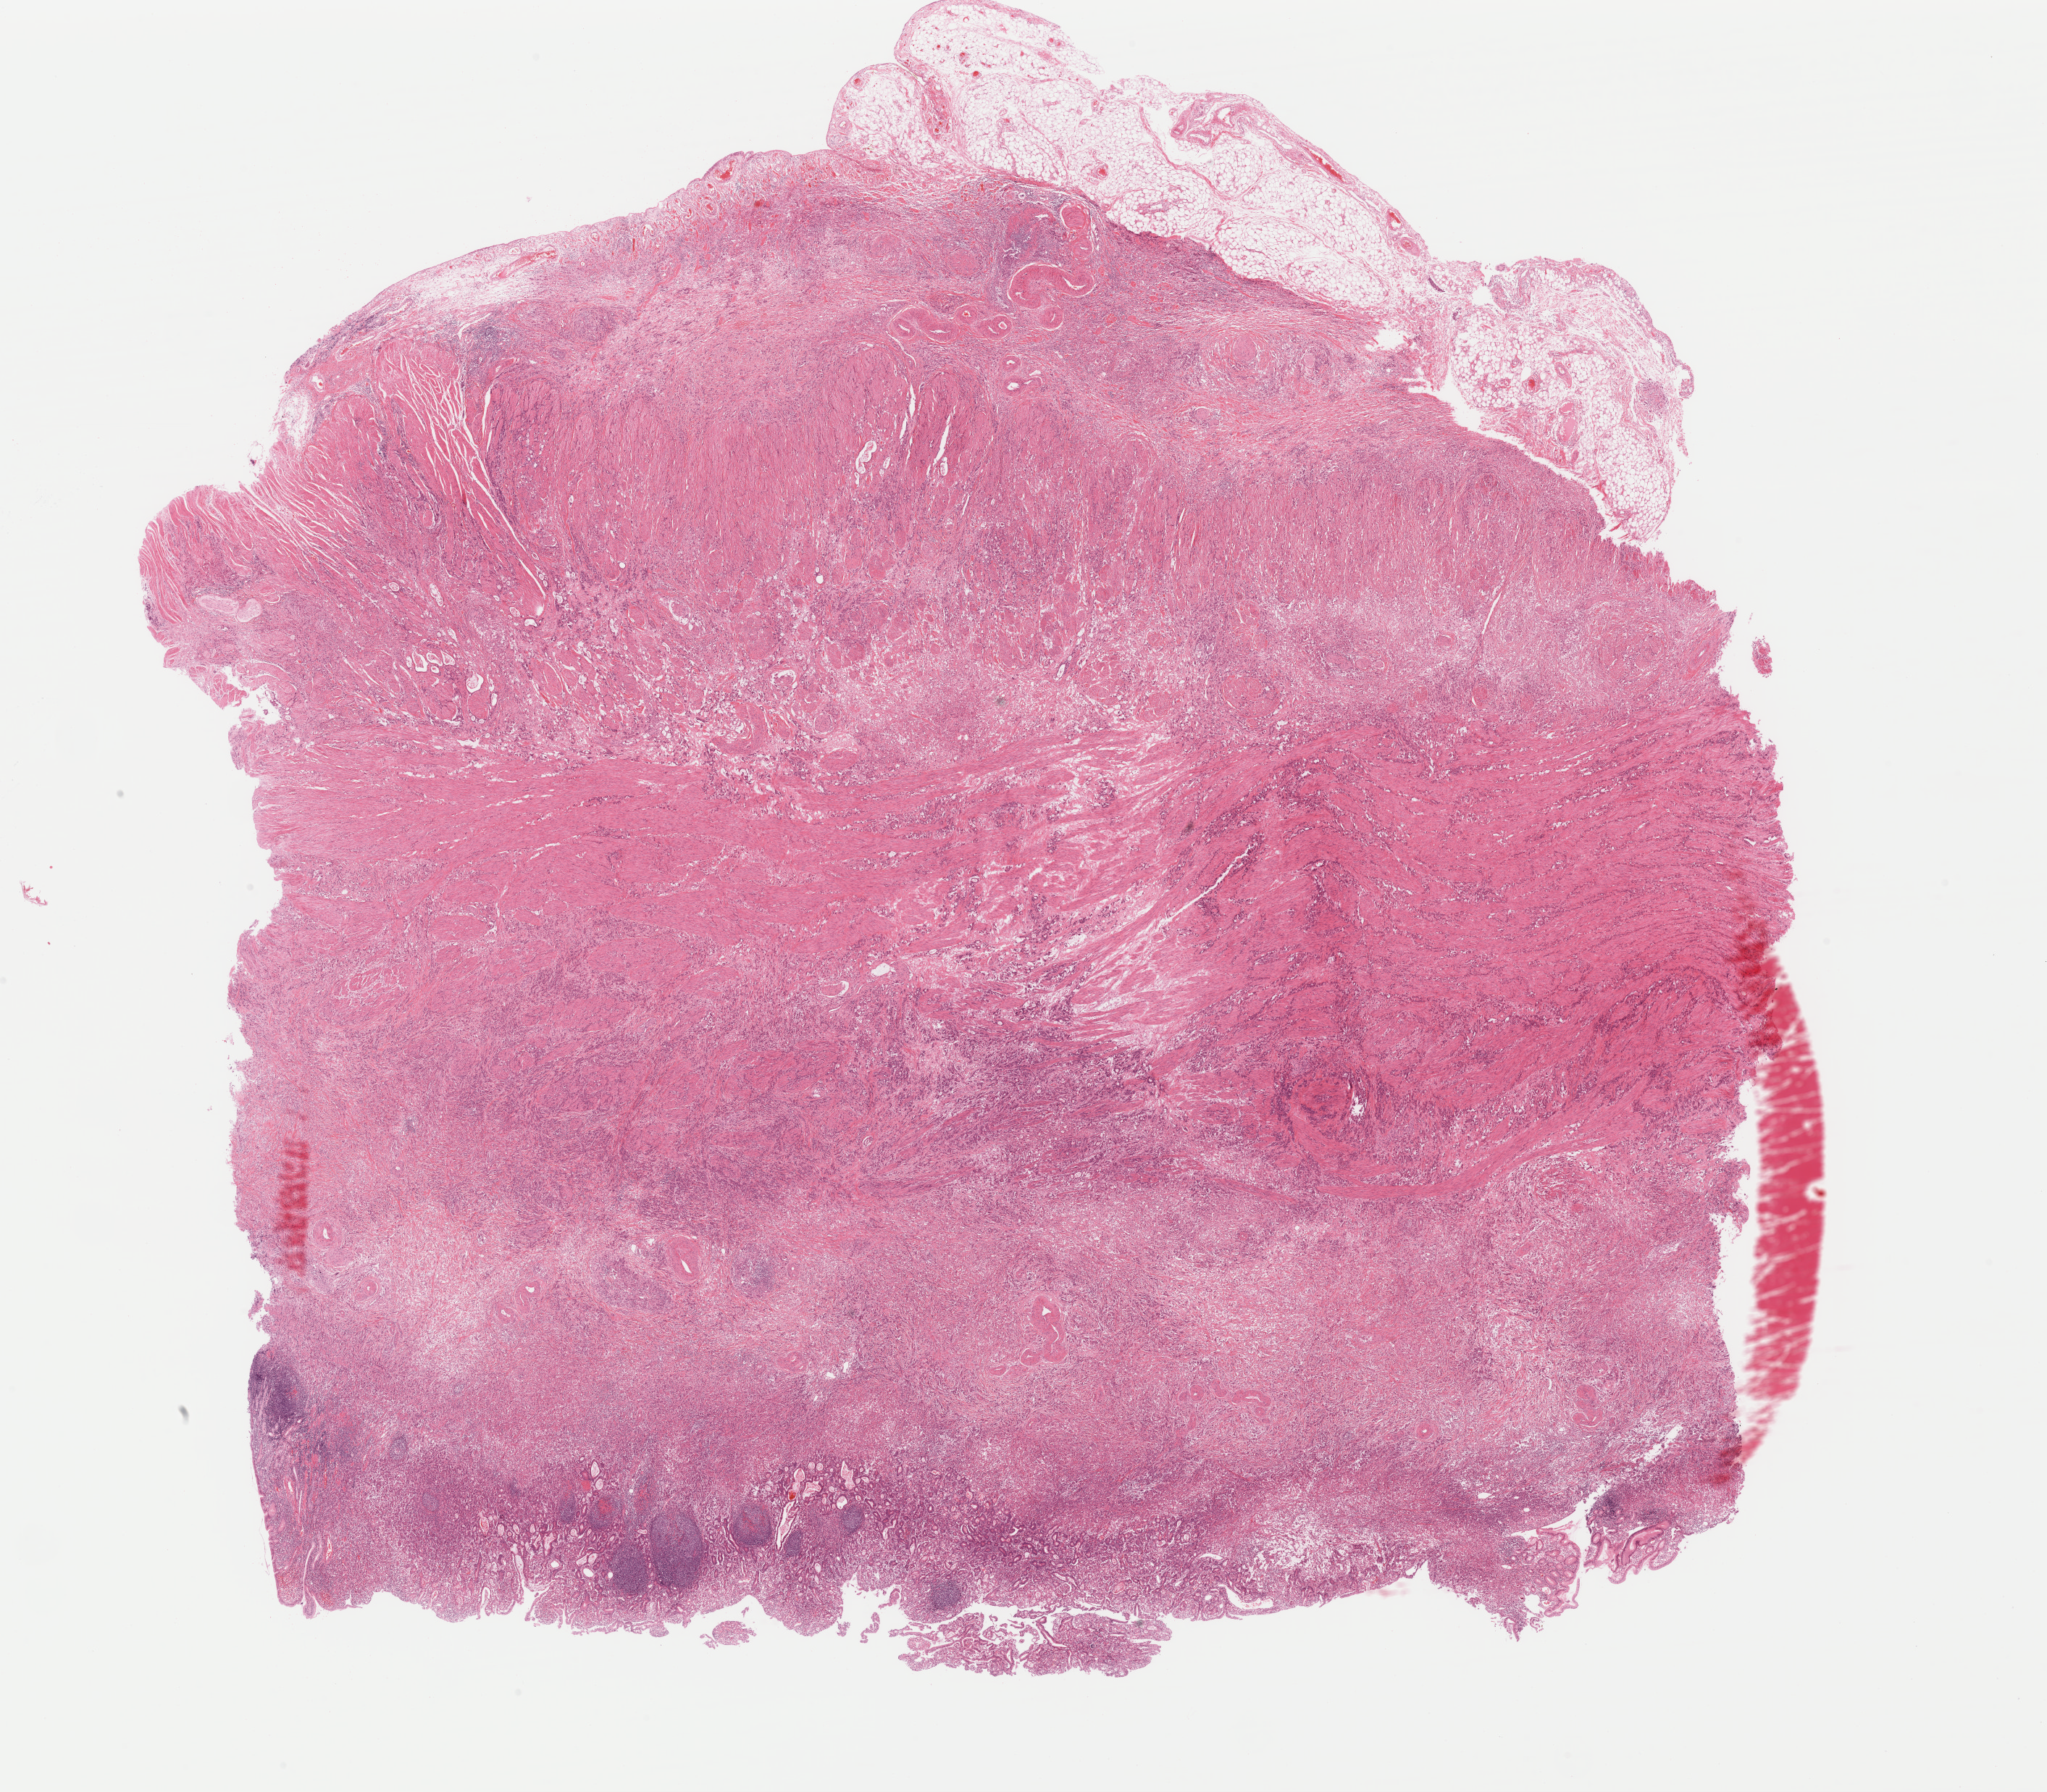
Whole-slide histology image, Hematoxylin and eosin (H&E) stained — a low-resolution overview of the entire scanned area, about 22.3 x 19.5 mm (acquisition: 40x scan), FFPE section, primary tumour sample from the stomach. Male, age 65 years at initial diagnosis. Histologic grade: G3 (poorly differentiated).
• histologic diagnosis: Adenocarcinoma, NOS (cardia, NOS)
• lymph nodes positive (case pathology): 6 of 6 examined
• AJCC pathologic stage: IIIA (7th edition)